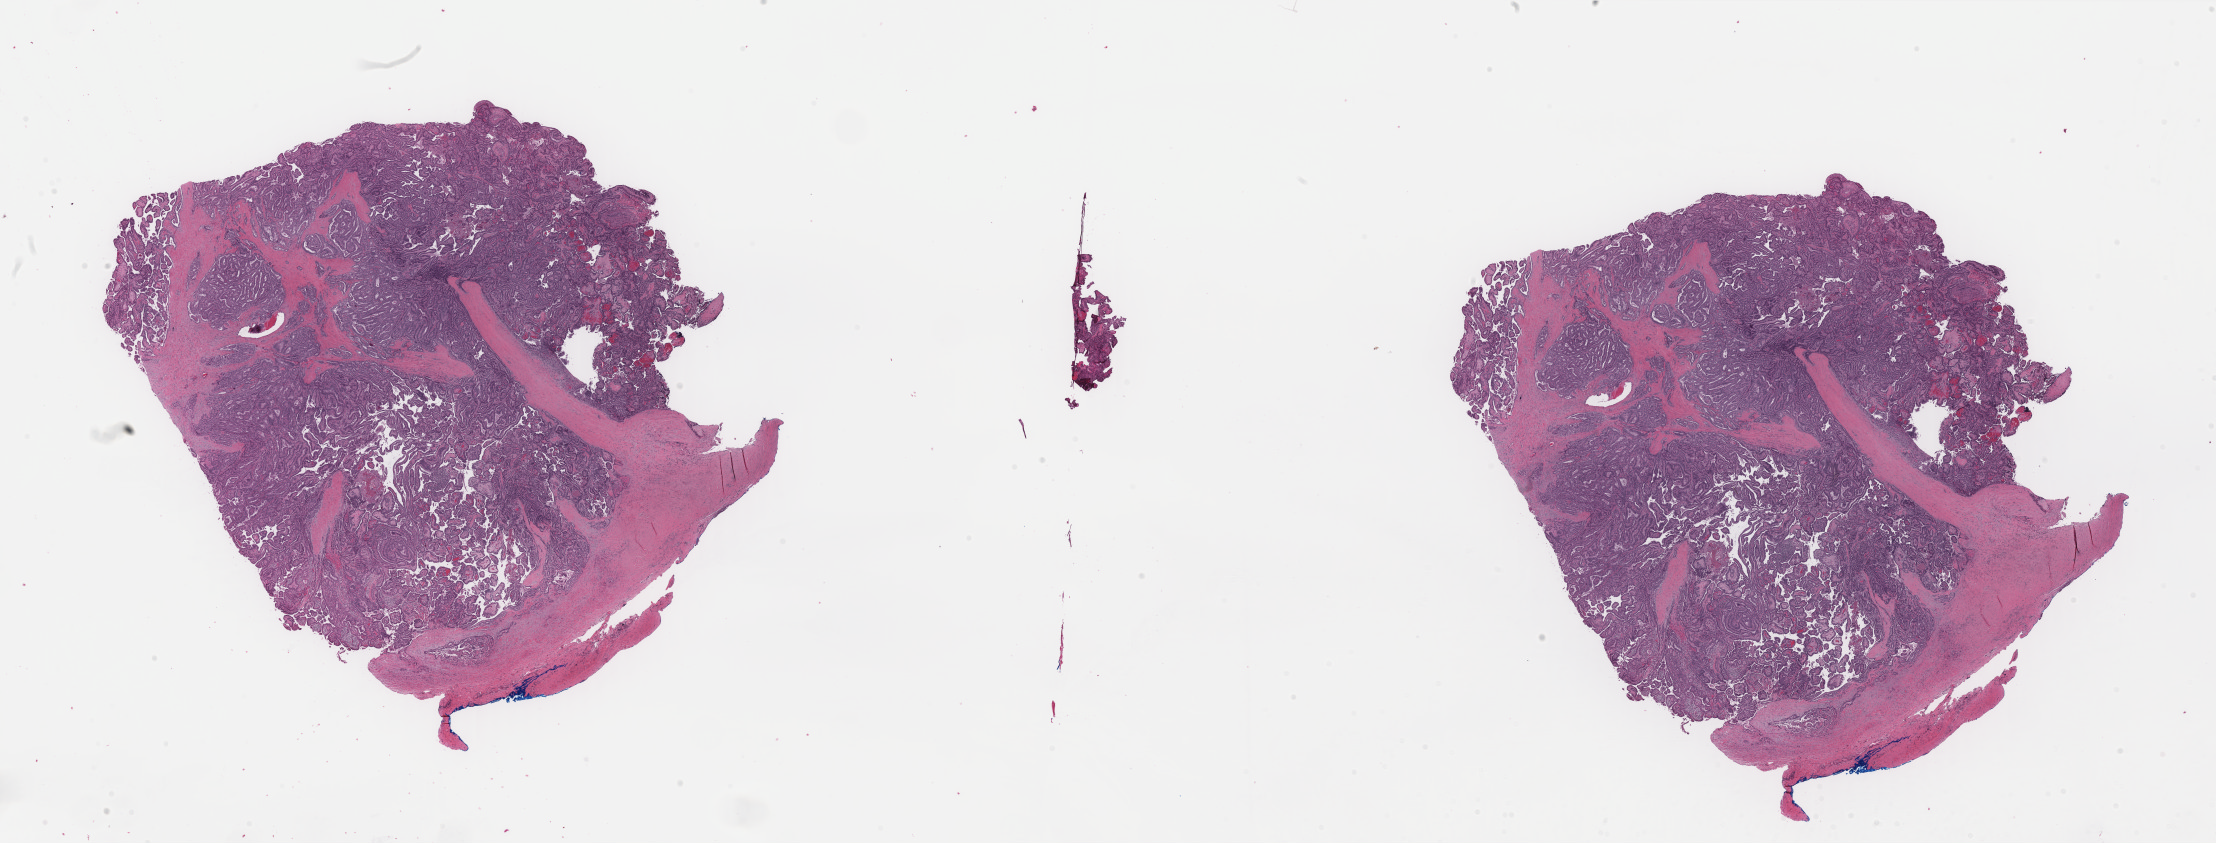
Whole-slide histology image, H&E-stained — whole scanned area (about 35.1 x 13.3 mm) shown as a low-resolution overview, FFPE section, primary tumour sample from the thyroid. Patient: female, age at initial diagnosis 34 years.
• pathologic diagnosis: Papillary adenocarcinoma, NOS (thyroid gland)
• laterality: right
• AJCC pathologic stage: I